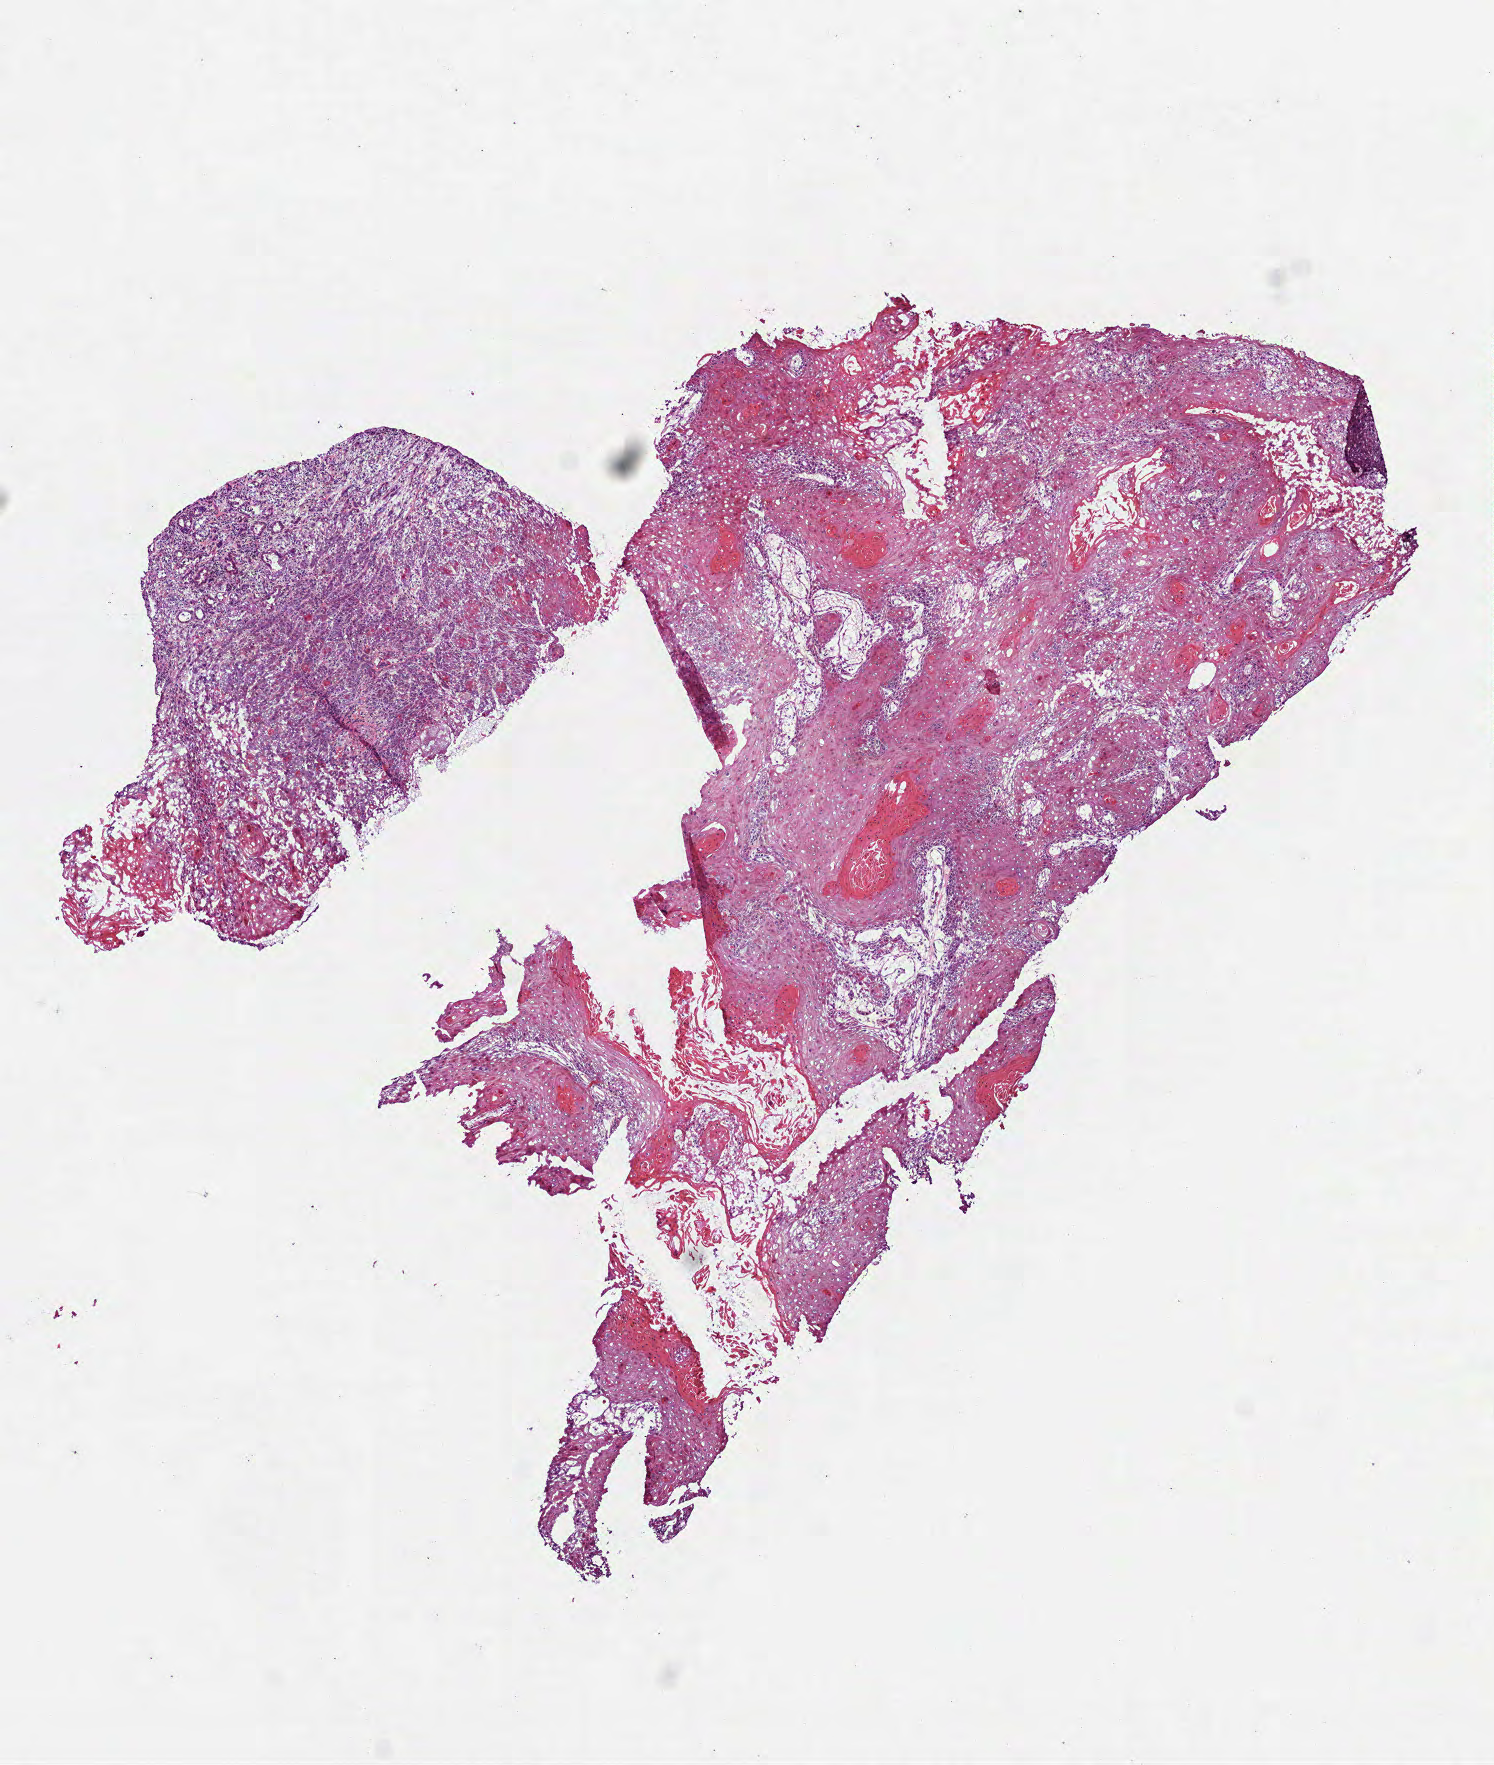
H&E-stained whole-slide image — a low-resolution overview of the entire scanned area, about 6.0 x 7.1 mm (acquisition: 40x scan); frozen section from the top of the tissue portion; primary tumour sample from the head and neck. Patient: female, age at initial diagnosis 52 years. Histologic grade: G2 (moderately differentiated). Composition of this section per pathologist review: tumour cells 90%, tumour nuclei 85%, normal cells 0%, stromal cells 10%, necrosis 0%.
• TNM: T3 N2b
• diagnosis: Squamous cell carcinoma, NOS (tongue, NOS)
• AJCC pathologic stage: IVA (6th edition)
• laterality: right